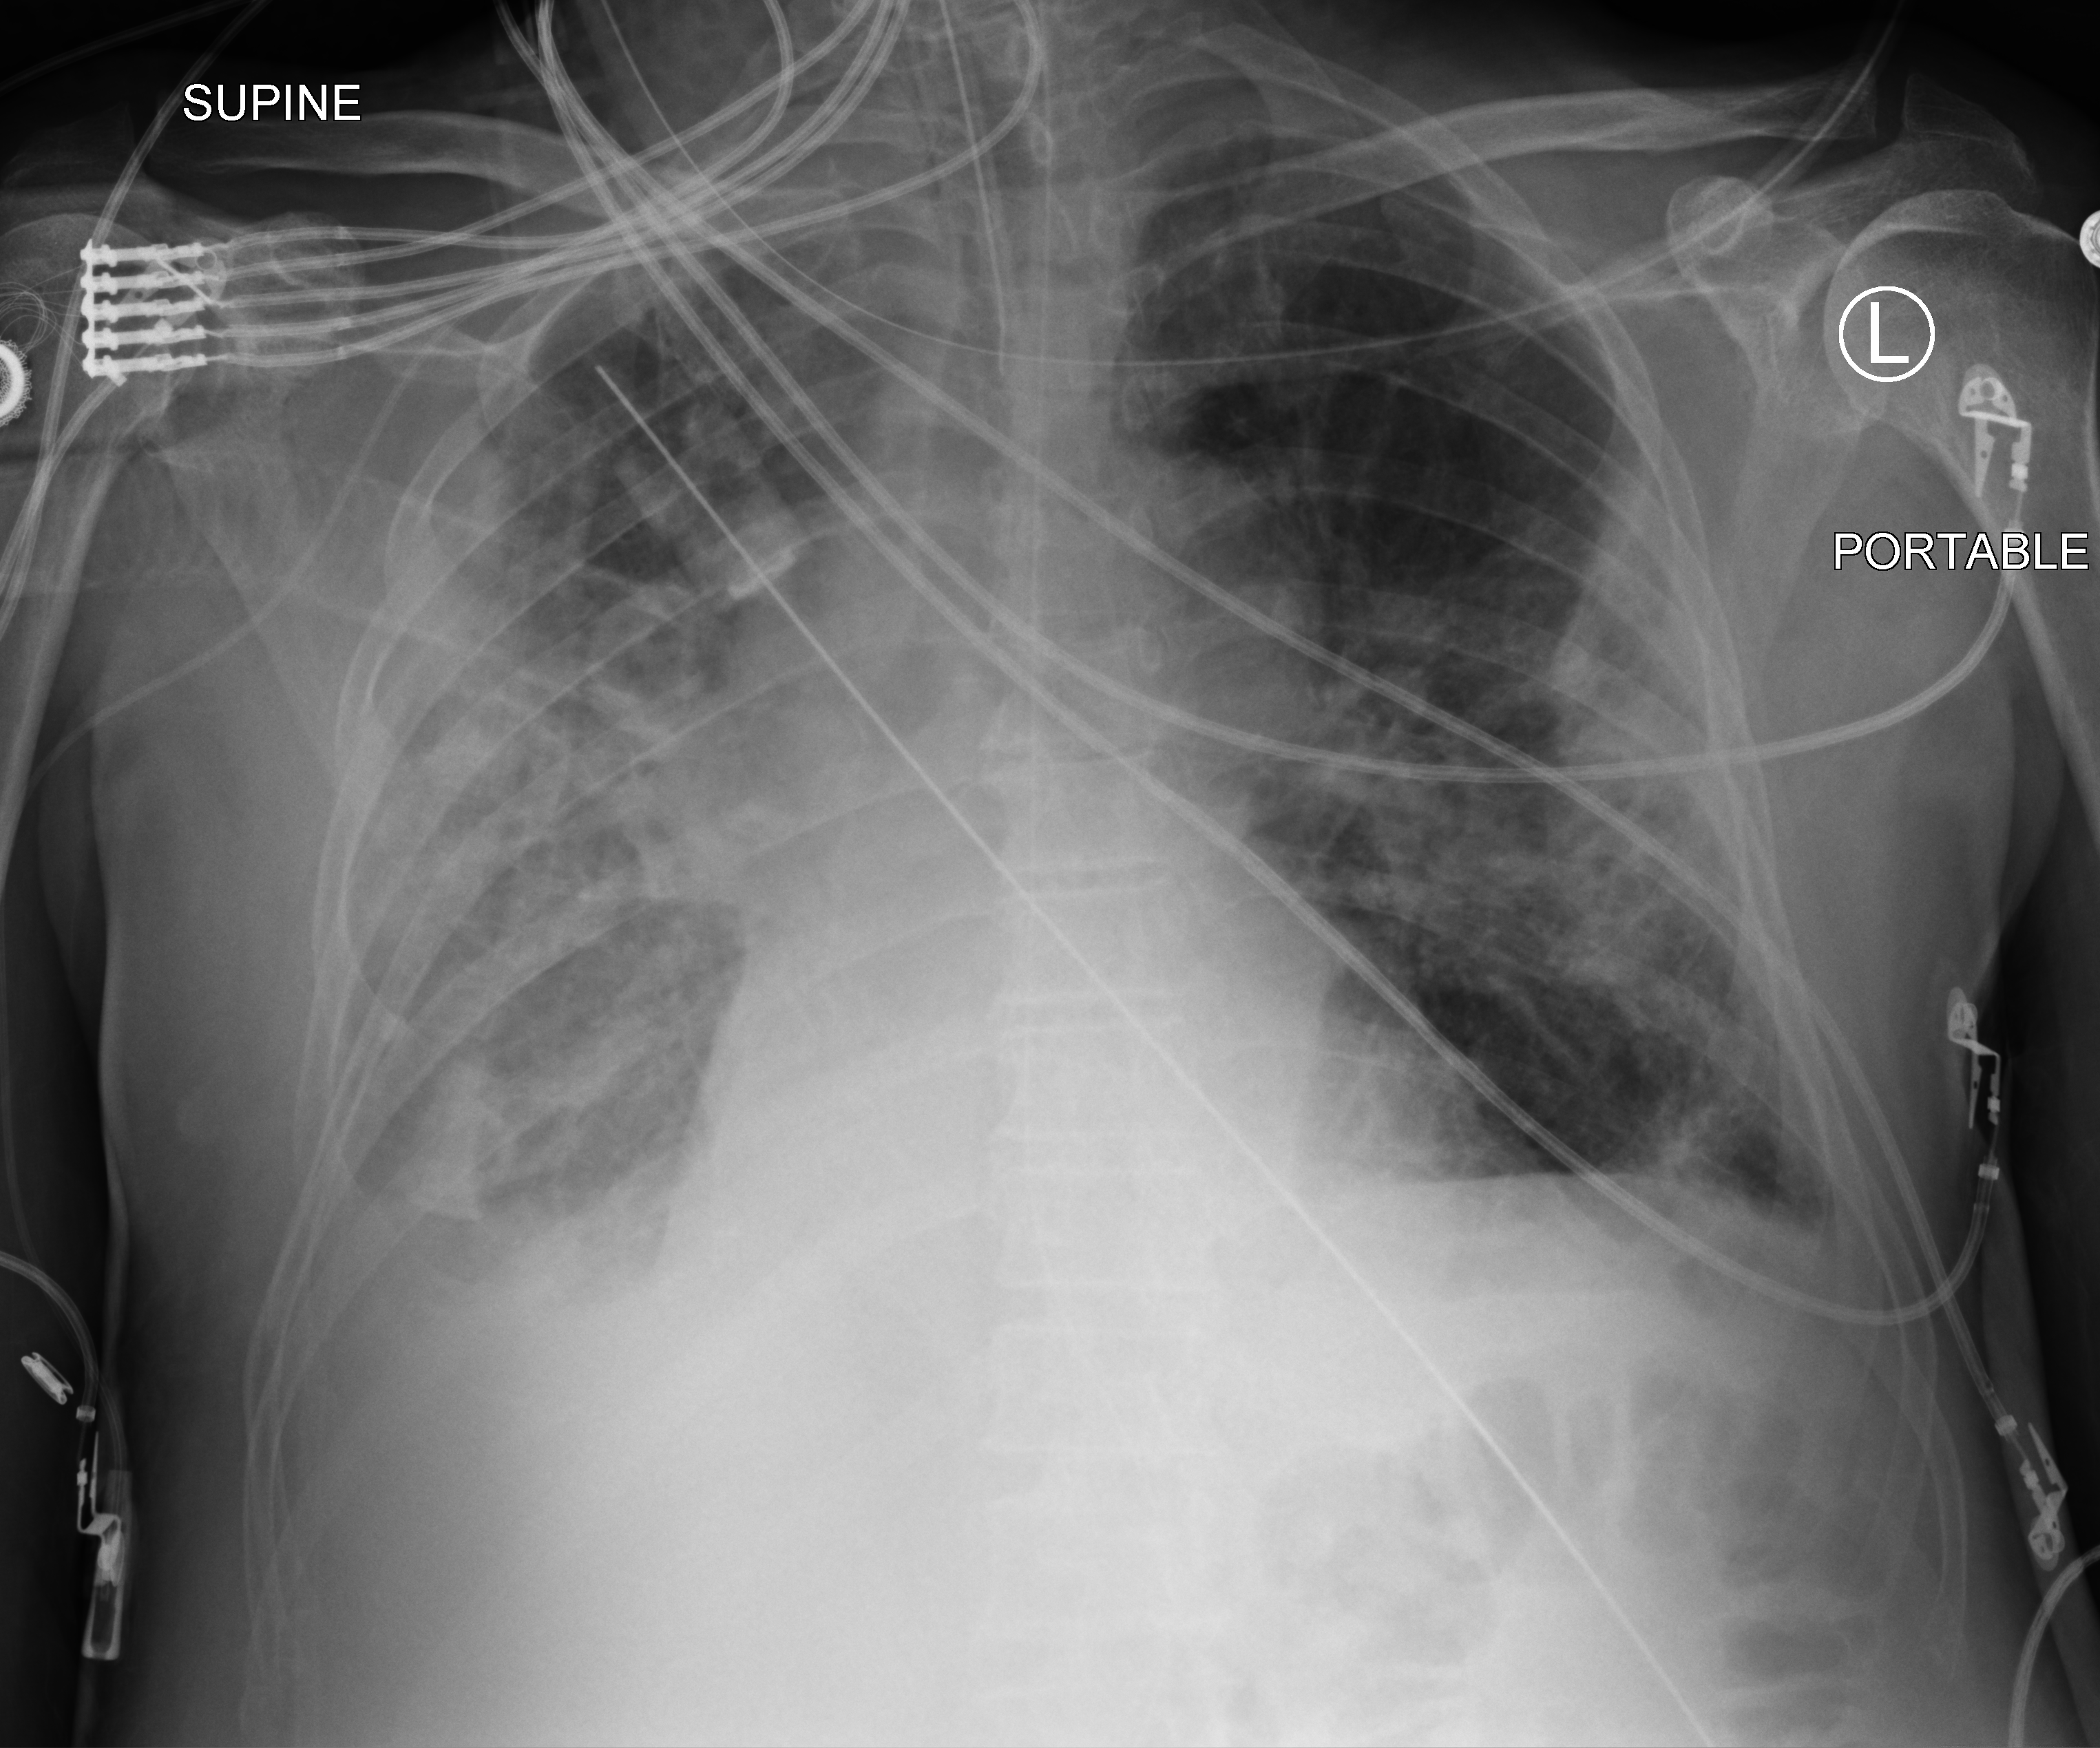
Chest X-ray (portable); anteroposterior (AP) projection. Patient hospitalised with COVID-19; male, aged 75–90 years.
Hospital-stay facts (about this admission, not read from this image; timing relative to this image not recorded):
- other chronic lung disease (admission record): yes
- length of hospital stay: 70 days